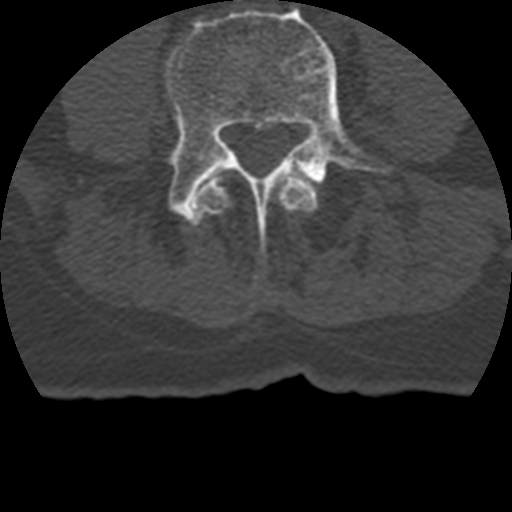
CT including the spine, one axial slice; reconstruction kernel STANDARD; bone window (W 1800 / L 400 HU); 512 × 512 image matrix, field of view 160 × 160 mm. Patient age 69 years. From the clinical record (not read from this slice): primary cancer: prostate.
Outlined on this slice (semi-automatic segmentation, software-assisted and operator-edited):
- L3 vertebra: bounding box [x1, y1, x2, y2] px = [196, 175, 319, 215]
- L4 vertebra: [164, 6, 386, 234]